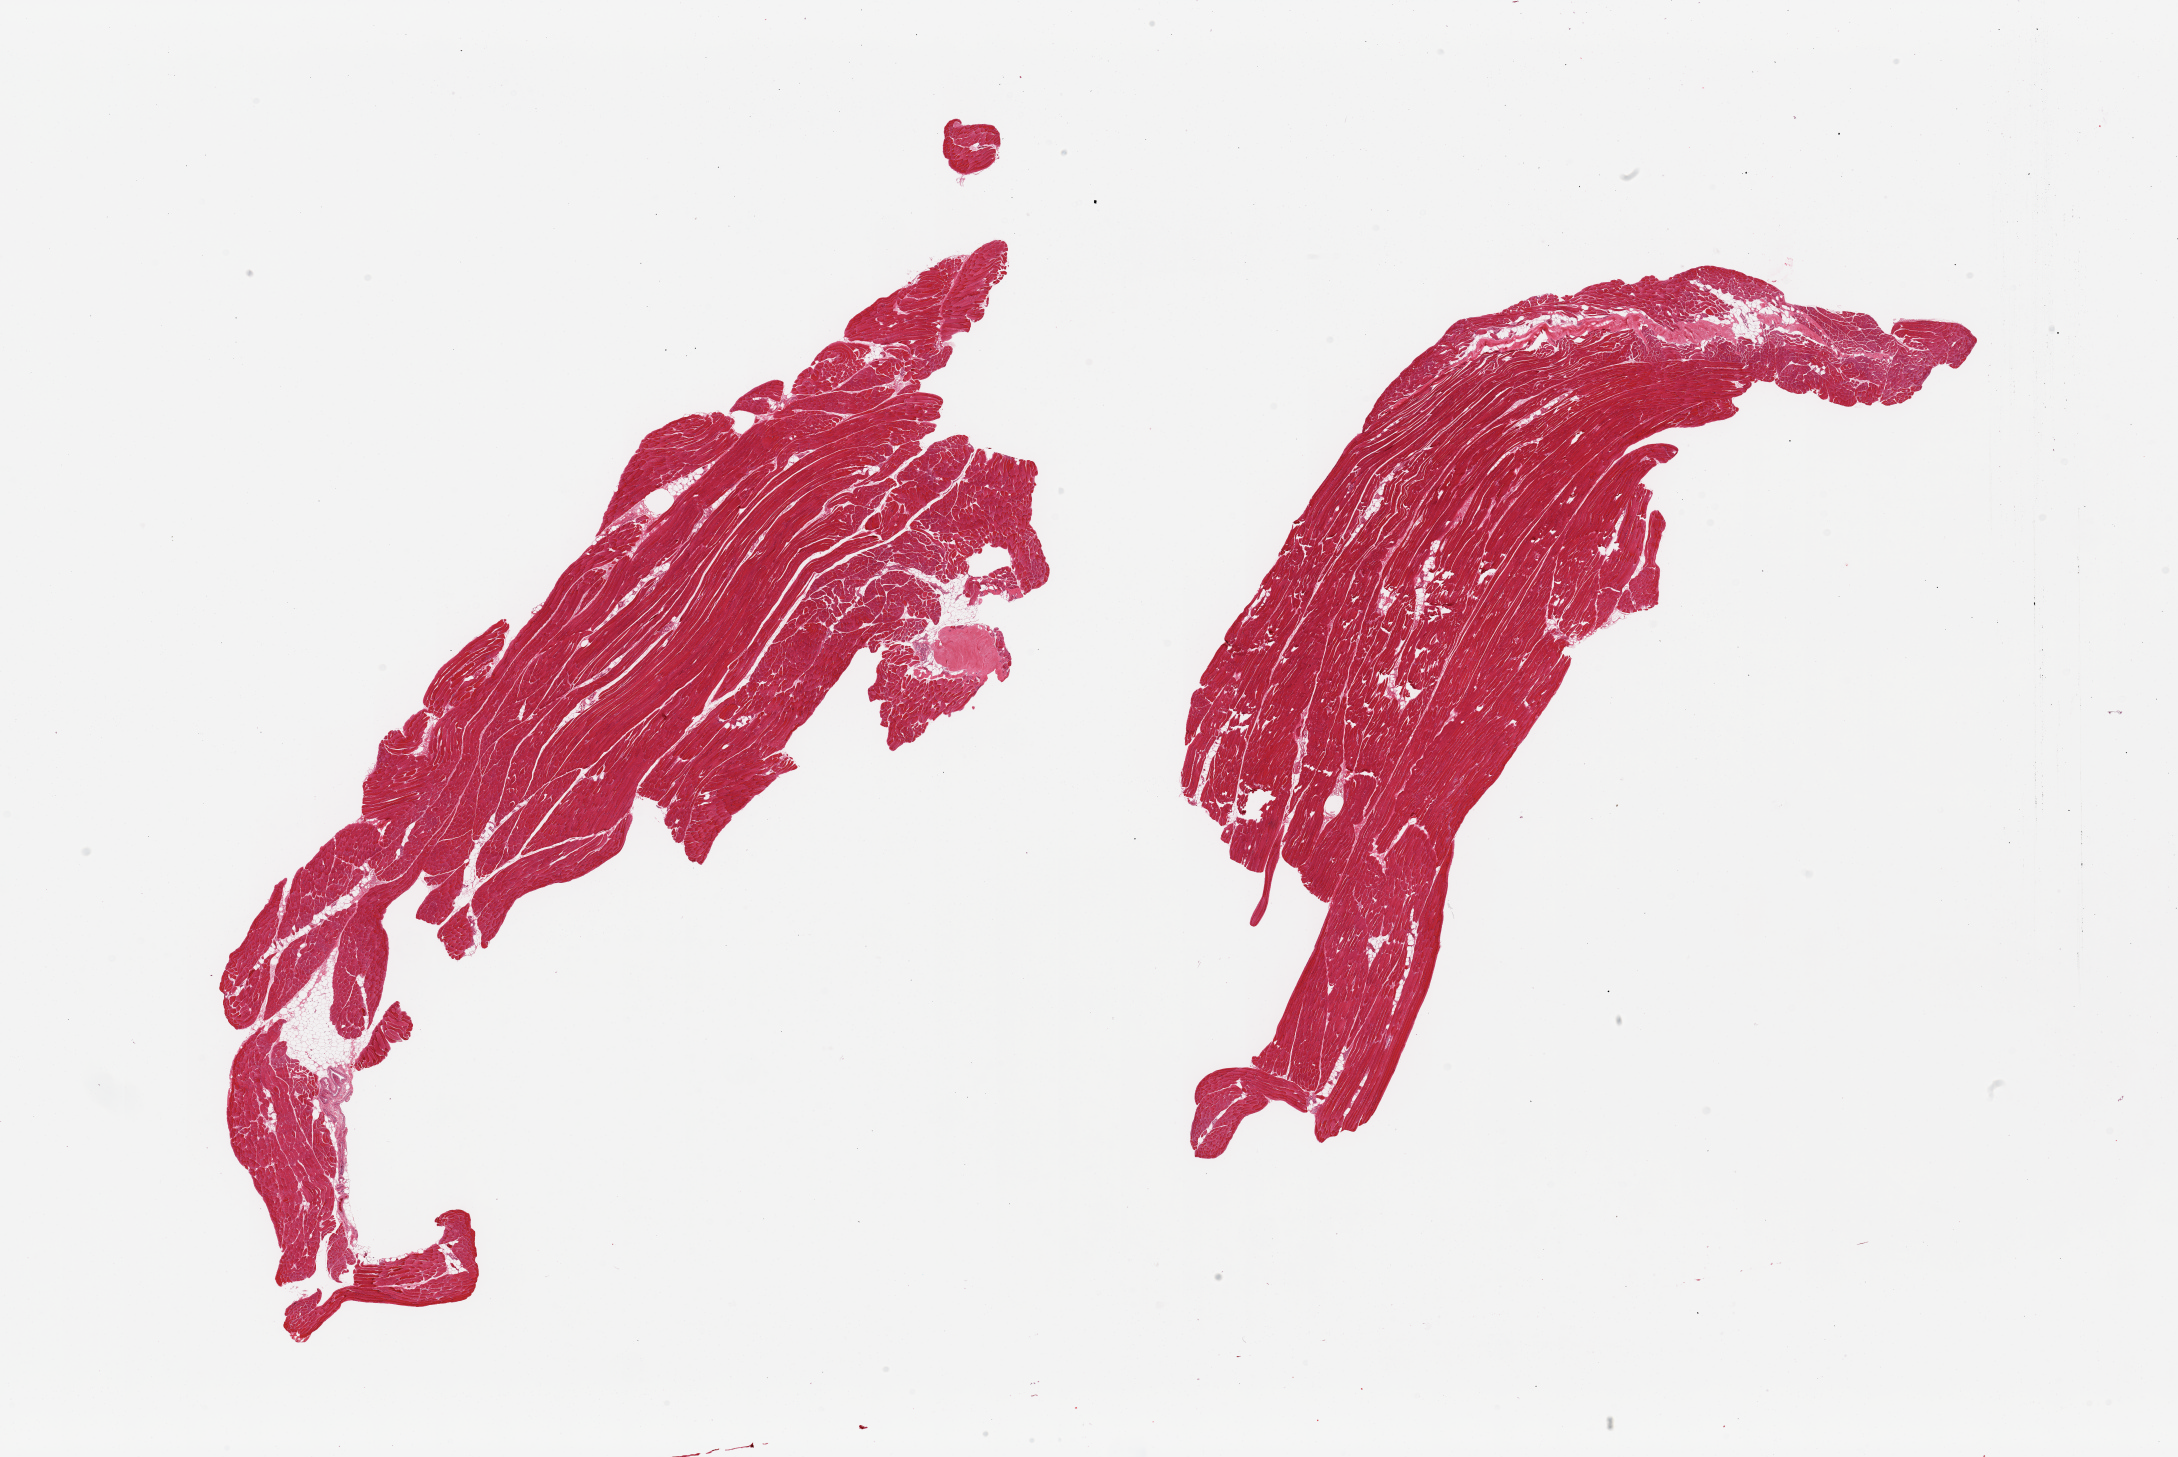
H&E whole-slide image — a low-resolution overview of the entire scanned area, about 34.5 x 23.0 mm (from a 20x scan). PAXgene-fixed paraffin-embedded (PFPE) section. Sampled site (target tissue): skeletal muscle. Donor tissue sample. Donor: male.
- review note (as recorded): 2 pieces